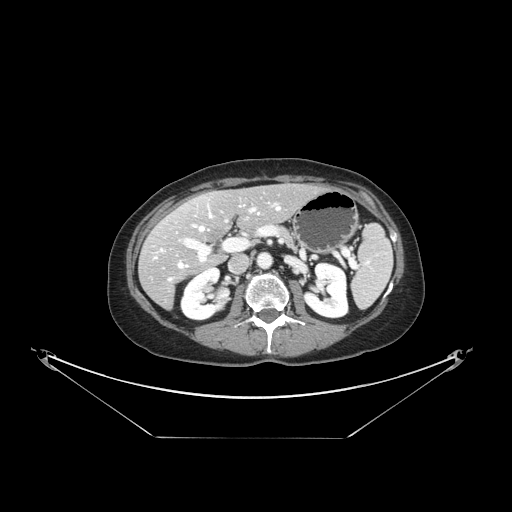
Contrast-enhanced abdominal CT, one axial slice. 120 kVp. Intravenous contrast given. Soft-tissue window (W 400 / L 40 HU). 2.5 mm slice thickness. 512 × 512 image matrix. Female patient, age 73 years. Case-level facts recorded for this patient, not image findings: diagnosis: colorectal cancer liver metastases, imaged before liver resection; multiple liver metastases: no.
Annotated regions visible in this slice (outlined manually by an expert reader):
- hepatic veins: bounding box [x1, y1, x2, y2] px = [155, 204, 281, 281]
- liver: [141, 184, 319, 308]
- planned liver remnant (the part of the liver to remain after resection): [168, 184, 320, 242]
- portal vein (with intrahepatic branches): [179, 207, 260, 263]